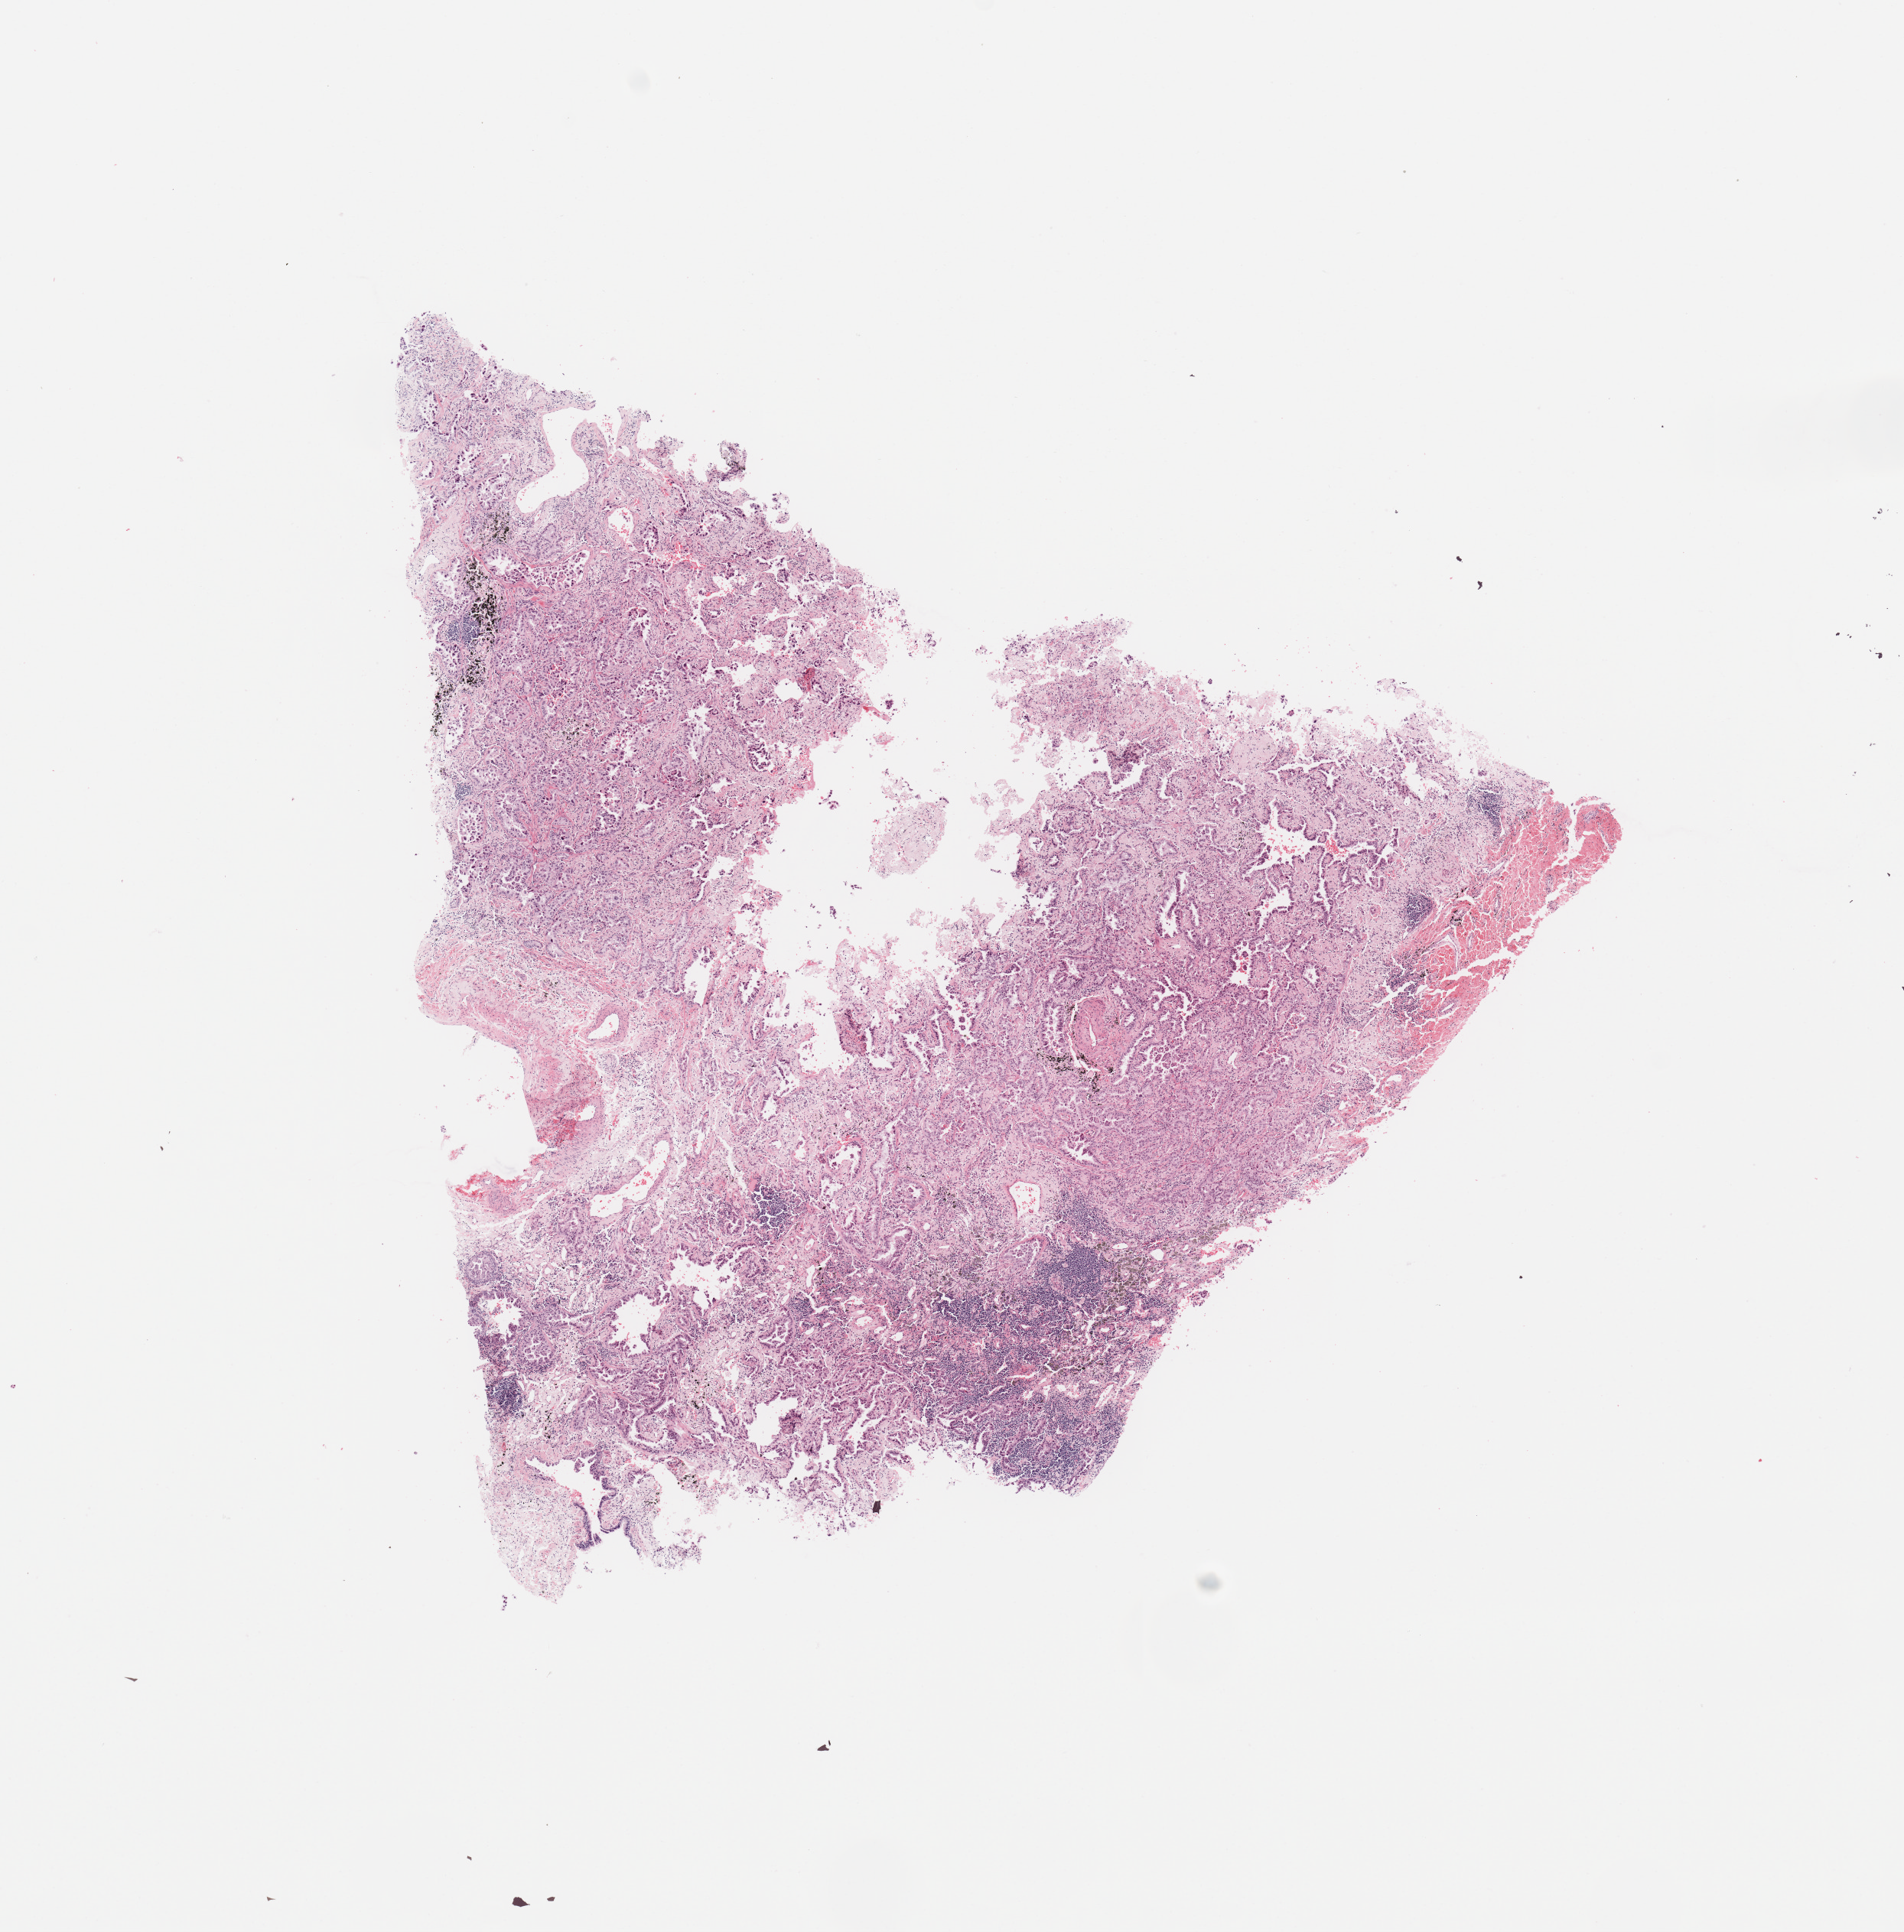
H&E-stained whole-slide image, a low-resolution overview of the entire scanned area, about 9.8 x 10.0 mm (from a 20x scan). Tumour tissue sample, sampled site: lung. Female, 50 y/o. Histologic grade: G2 (moderately differentiated). Composition of this section per pathologist review: tumour nuclei 65%, necrosis 5%.
Primary tumour site (as recorded): left lower lobe. Diagnosis: Adenocarcinoma, NOS. AJCC pathologic stage: IA3.